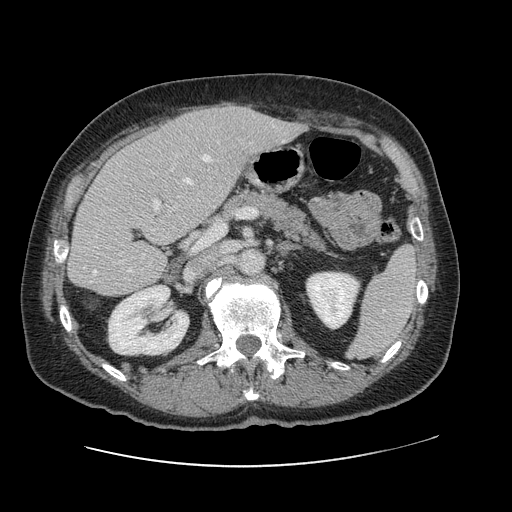
Contrast-enhanced abdominal CT, one axial slice. Position 55 of 138 along the scan axis. Intravenous contrast given. Soft-tissue window (W 400 / L 40 HU). 2.5 mm slice thickness. 512 × 512 image matrix, field of view 402 × 402 mm. Male patient, age 71 years. Case-level facts recorded for this patient, not image findings: diagnosis: colorectal cancer liver metastases, imaged before liver resection; multiple liver metastases: no.
Outlined on this slice (expert manual segmentation):
- hepatic veins: bounding box (x1, y1, x2, y2) in pixels: (93, 155, 227, 275)
- liver: (70, 106, 301, 295)
- planned liver remnant (the part of the liver to remain after resection): (70, 143, 200, 295)
- portal vein (with intrahepatic branches): (153, 199, 160, 211)